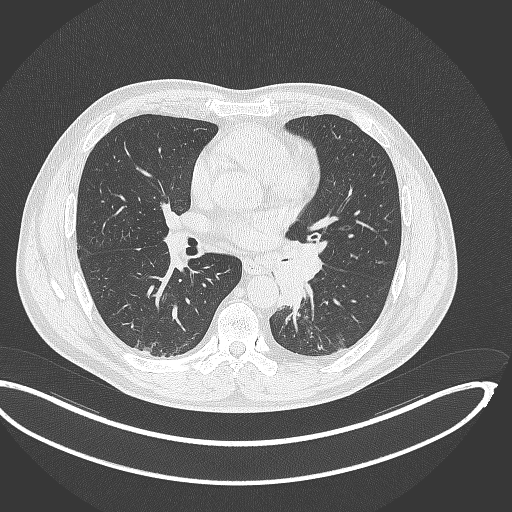
Chest CT, one axial slice; slice 182 of 362 in the series (ordered by position); reconstruction kernel B70f; 120 kVp; lung window (W 1500 / L -600 HU); 512 × 512 image matrix, field of view 442 × 442 mm. Male patient, age 50 years. From the clinical record (not read from this slice): clinical TNM (as recorded): T2a N3 M0.
Structures marked on this image (bounding box drawn by a radiologist):
- lung tumour (recorded histology: squamous cell carcinoma): bounding box (x1, y1, x2, y2) in pixels: (267, 249, 325, 315)